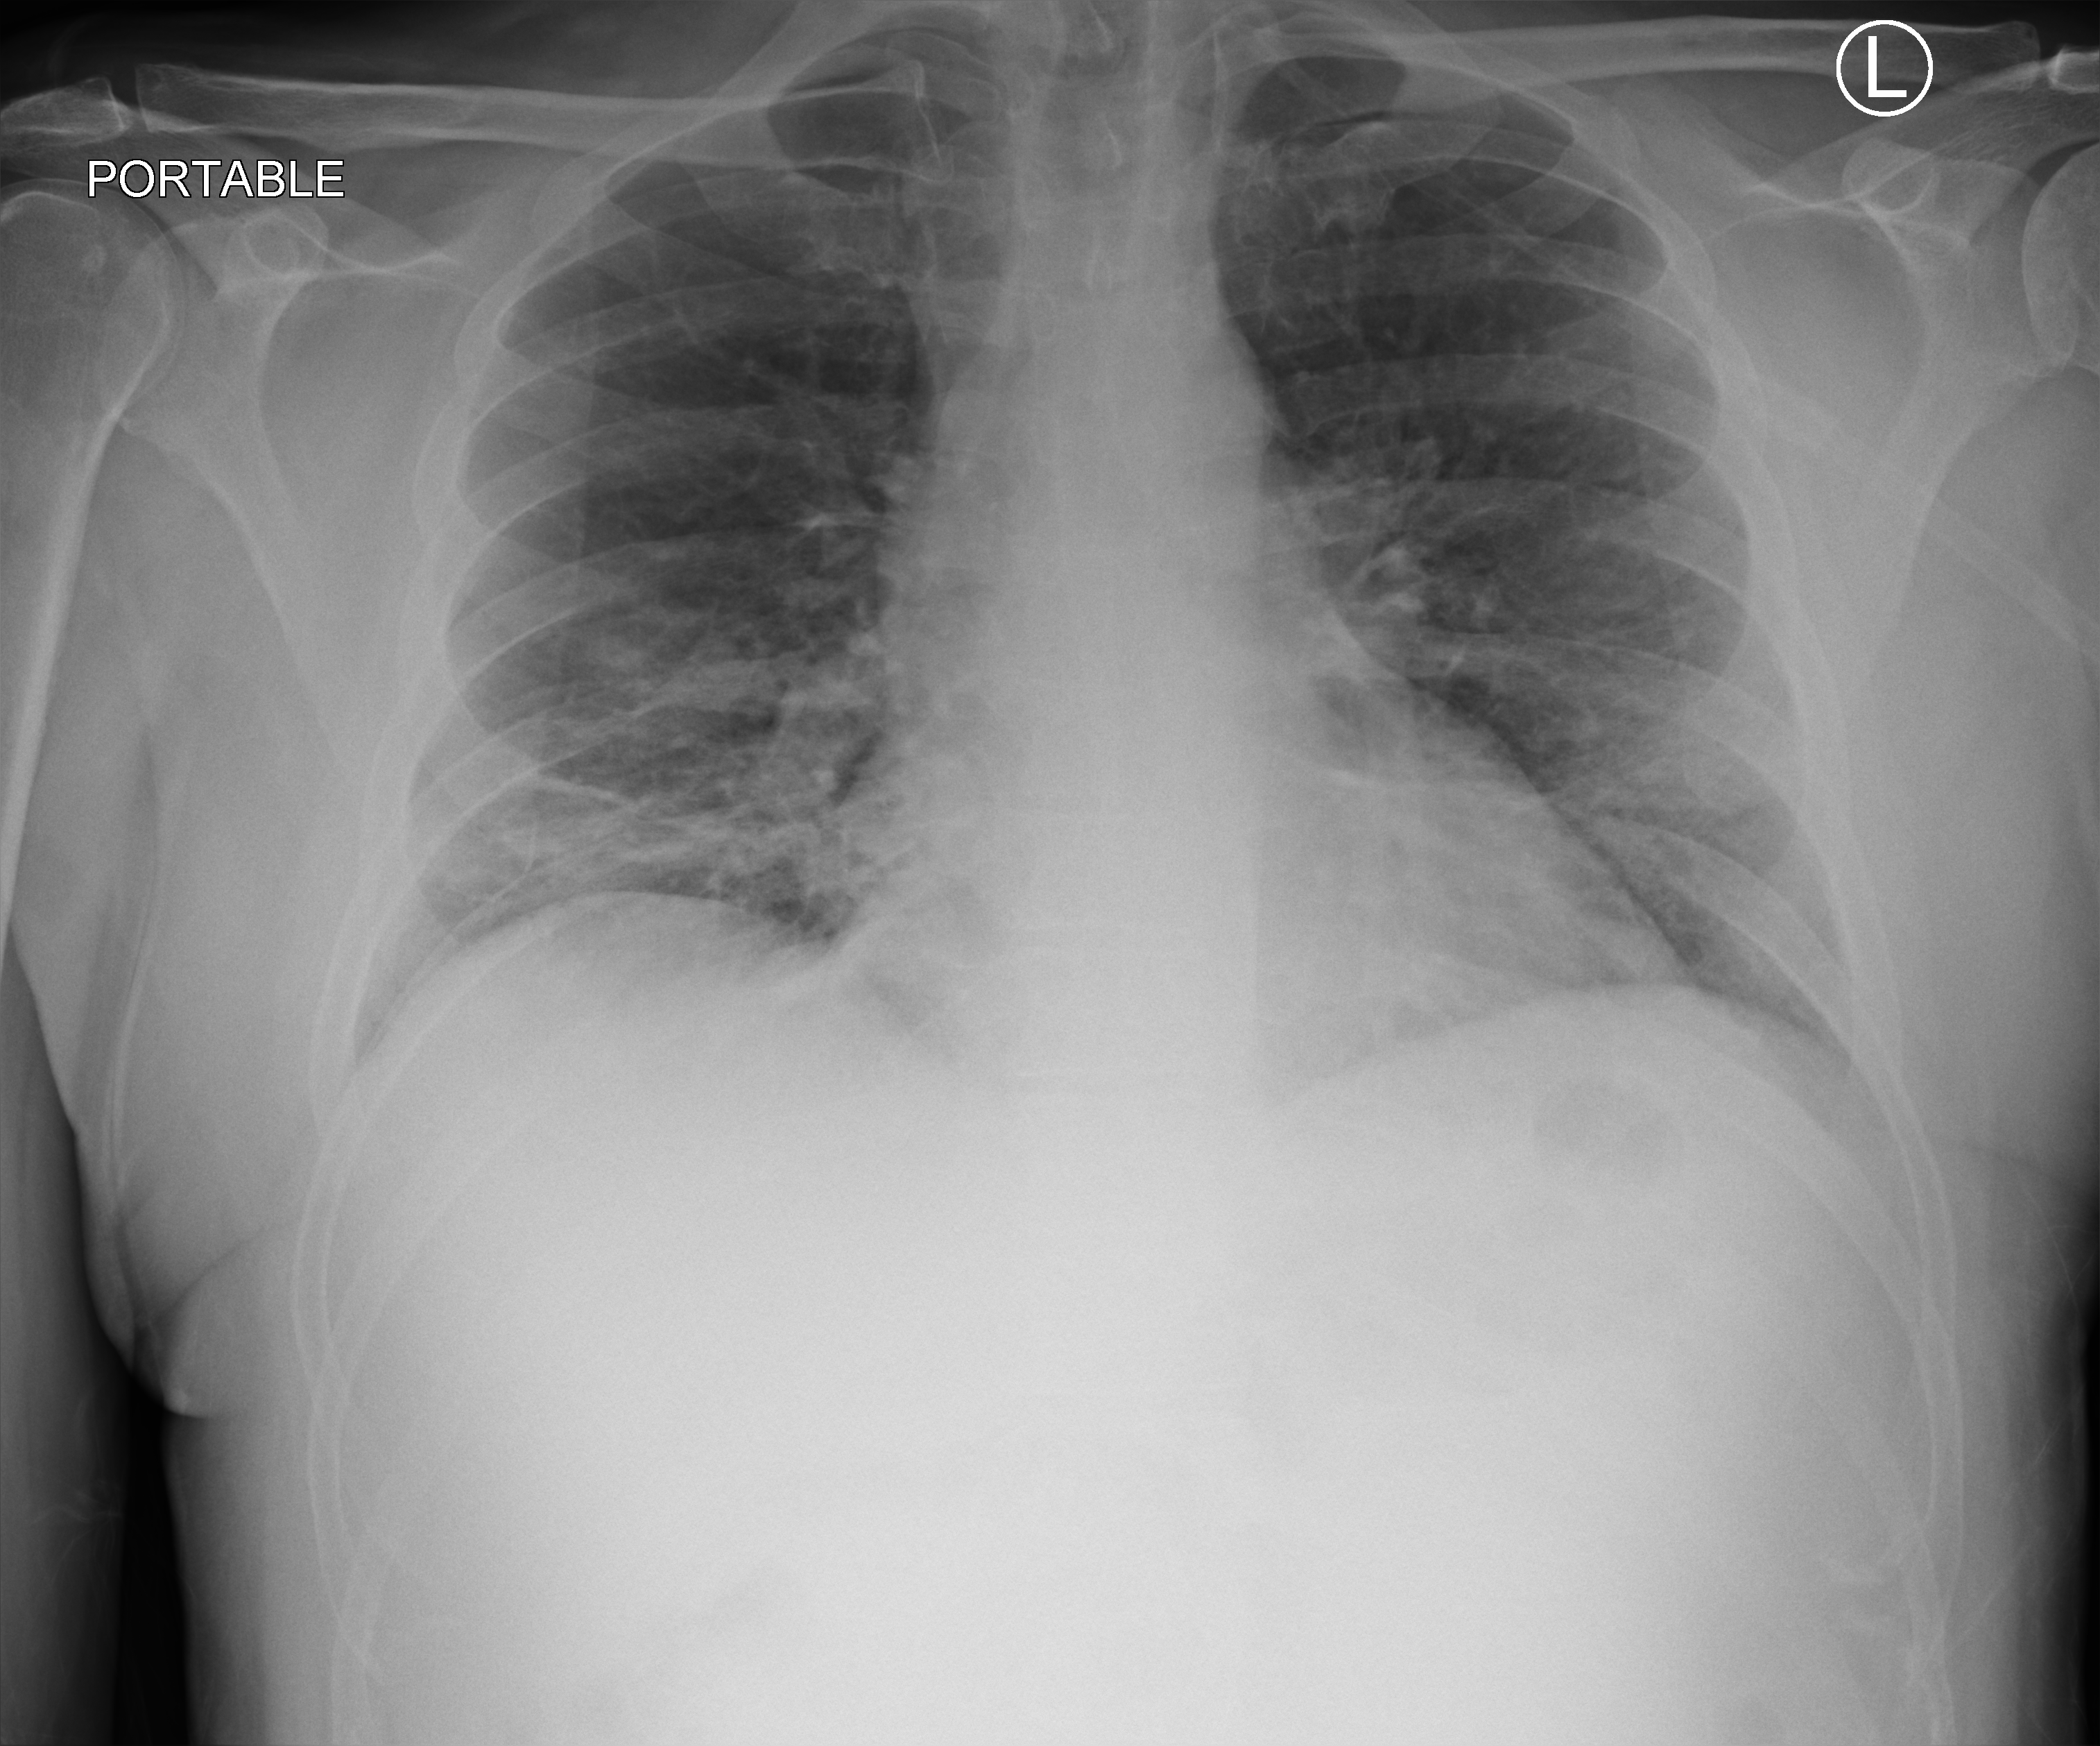
Portable chest radiograph; anteroposterior (AP) projection. Male patient hospitalised with COVID-19, age 18–59 years.
Hospital-stay facts (about this admission, not read from this image; timing relative to this image not recorded): admitted to intensive care during this hospital stay: no.